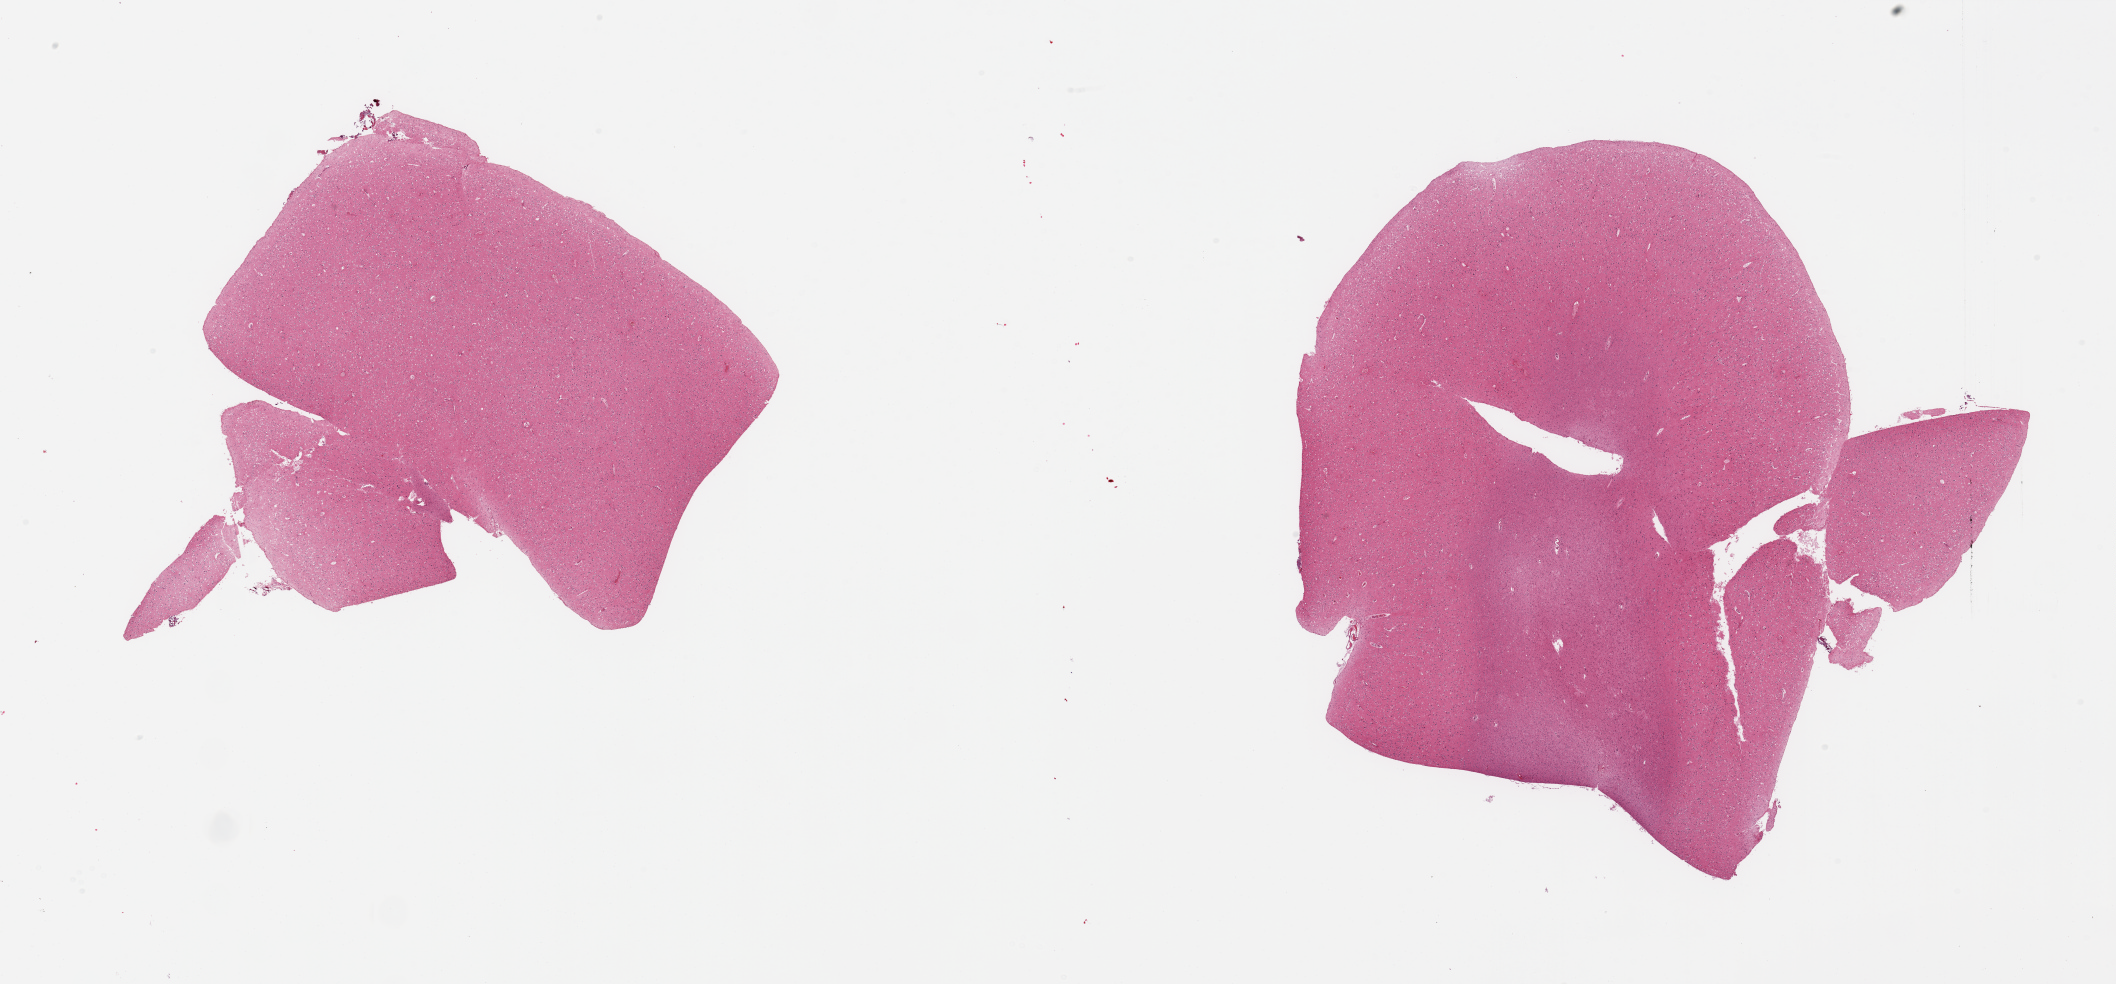
Hematoxylin and eosin (H&E) whole-slide image, brightfield, low-resolution overview of the scanned area, about 33.5 x 15.6 mm; PAXgene-fixed, paraffin-embedded tissue; sampled site (target tissue): cerebral cortex; tissue donor sample. Donor sex: male.
* pathologist's review note for this sample: 2 pieces, no abnormalities